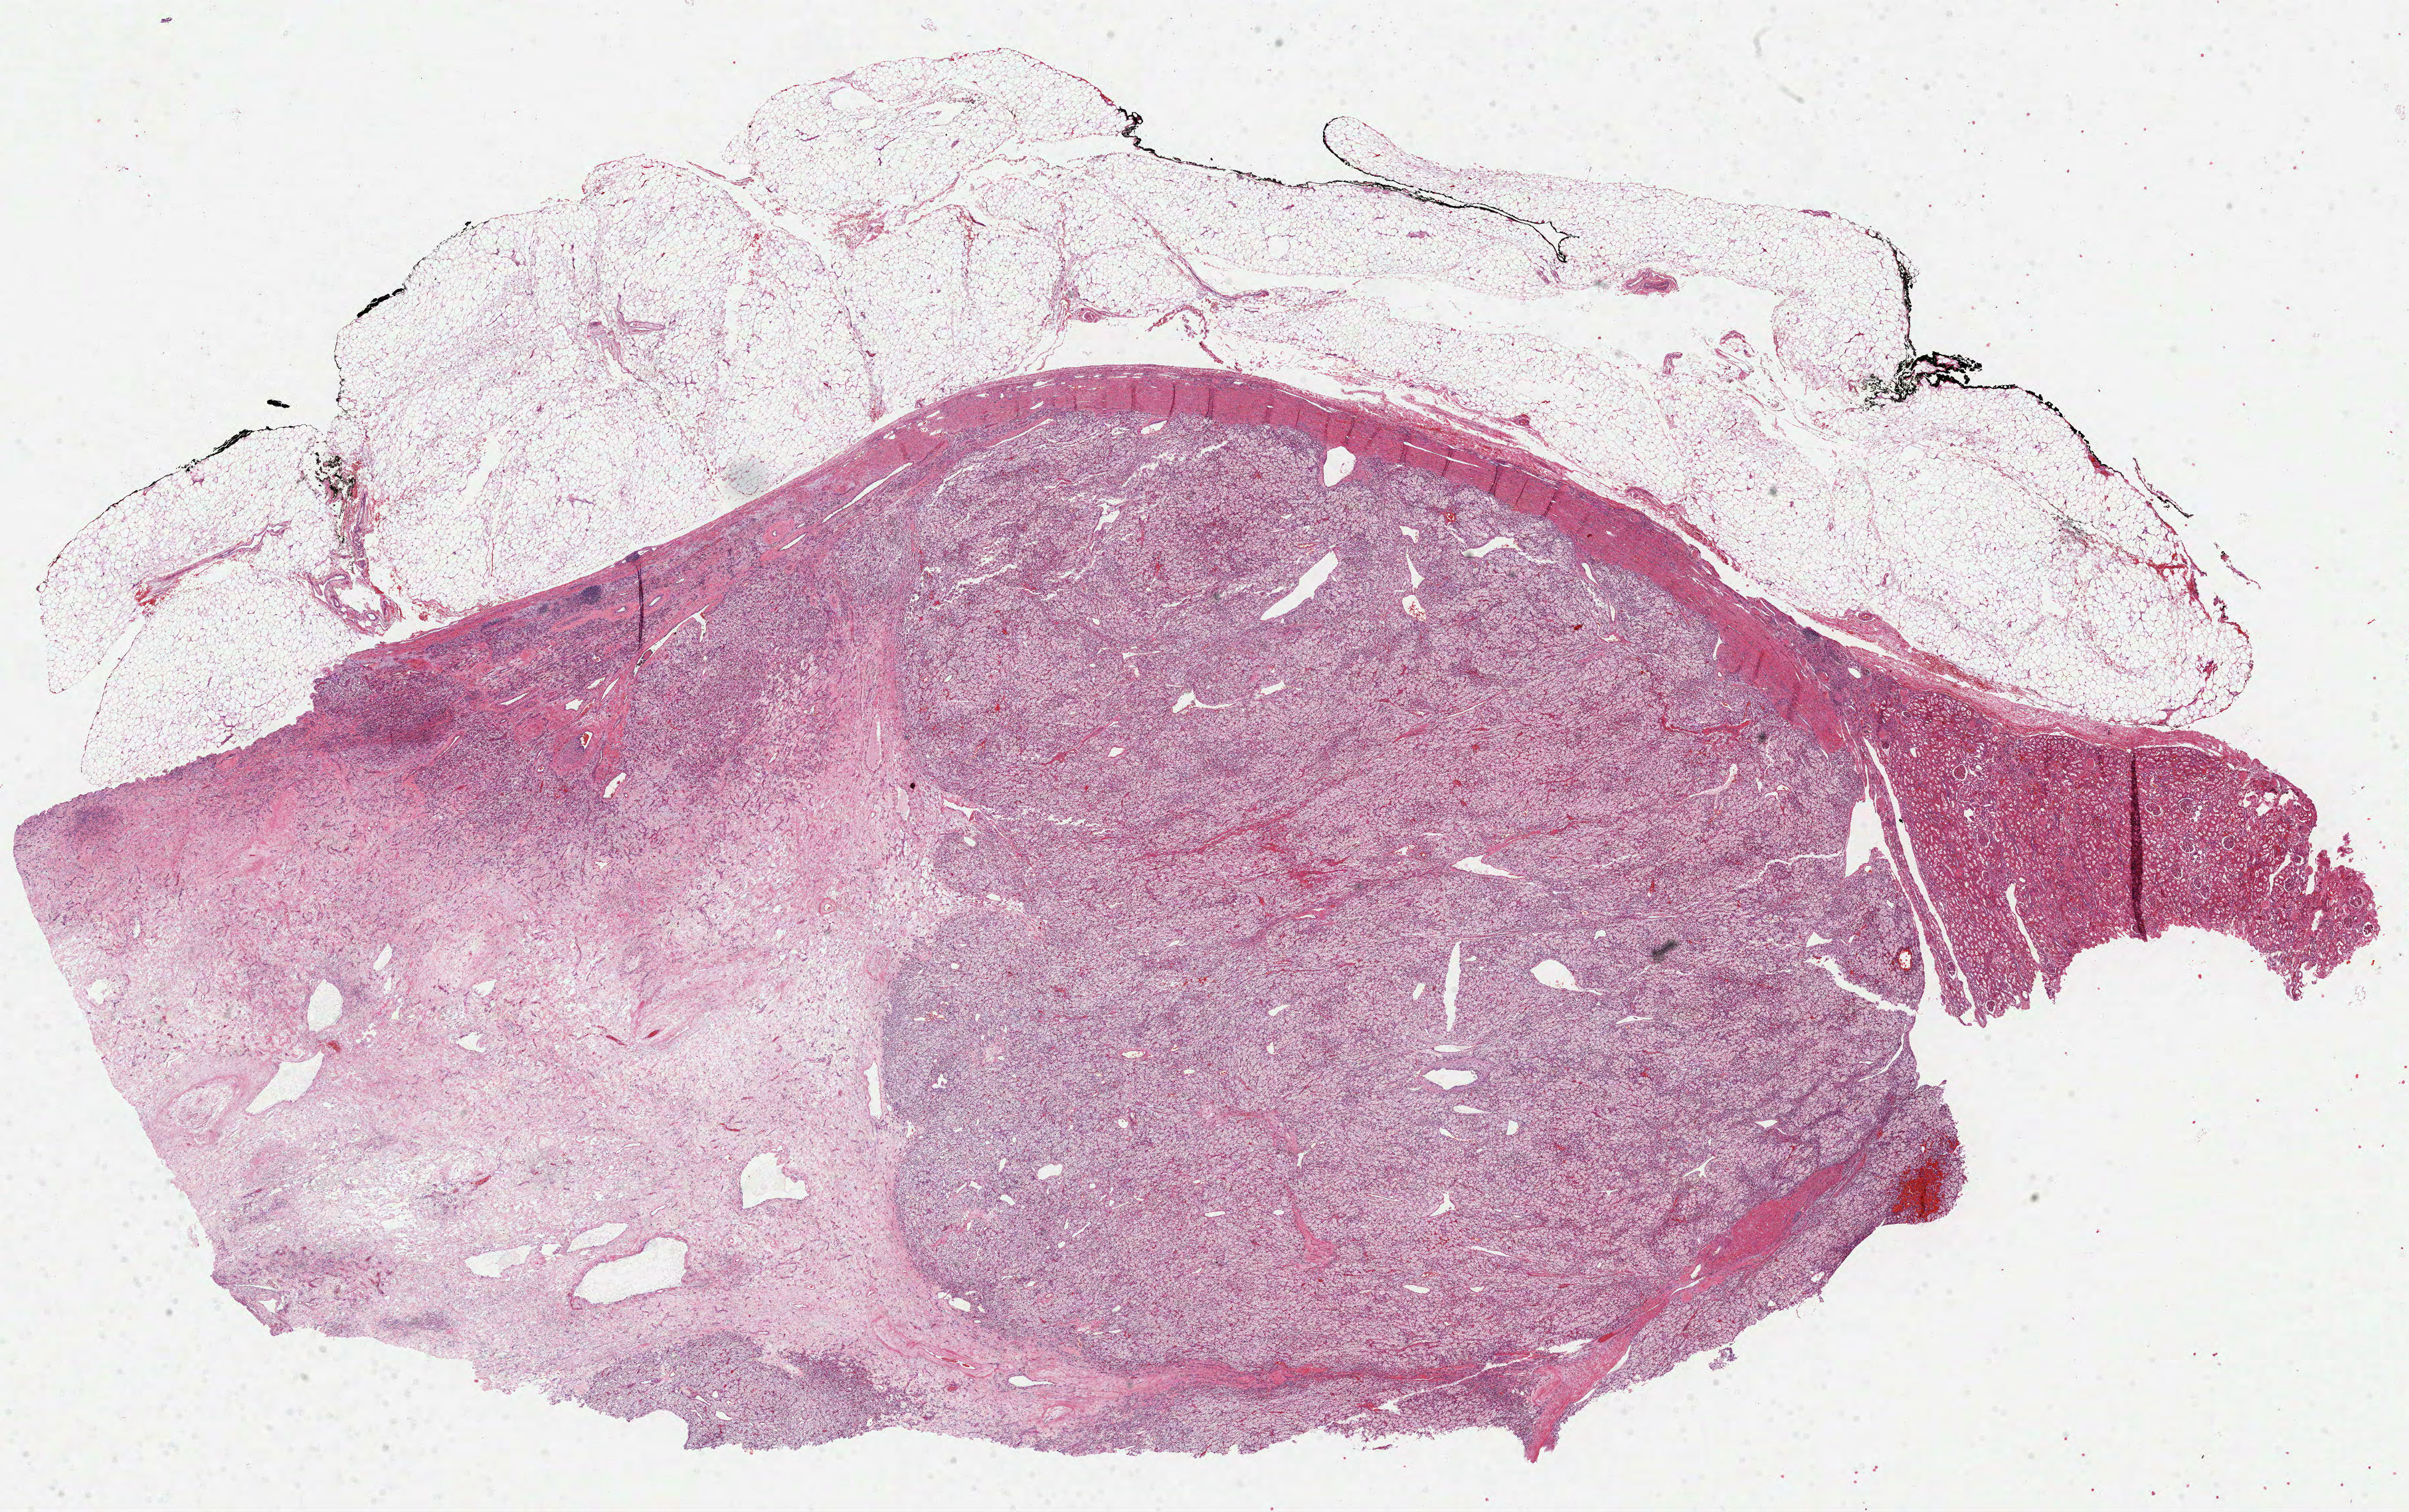
Digitized Hematoxylin and eosin (H&E) stained tissue section (whole slide), whole scanned area (about 29.2 x 18.4 mm, from a 40x scan) shown as a low-resolution overview. Formalin-fixed paraffin-embedded (FFPE) diagnostic section. Kidney, primary tumour sample. Female patient; age at initial diagnosis 61 years. Histologic grade: G2 (moderately differentiated).
AJCC pathologic stage: I. Laterality: left. Diagnosis: Clear cell adenocarcinoma, NOS.